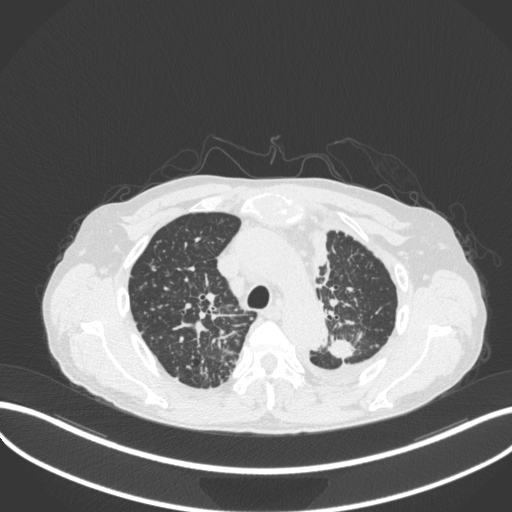
Chest CT, one axial slice. Slice 264 of 319 in the series (ordered by position). 120 kVp. Lung window (W 1500 / L -600 HU). 1 mm slice thickness. 512 × 512 image matrix, field of view 400 × 400 mm. Male patient, age 58 years. From the clinical record (not read from this slice): clinical TNM (as recorded): T1c N3 M1.
Annotated regions visible in this slice (bounding box drawn by a radiologist):
- lung tumour (recorded histology: adenocarcinoma): bounding box [x1, y1, x2, y2] px = [324, 334, 365, 364]